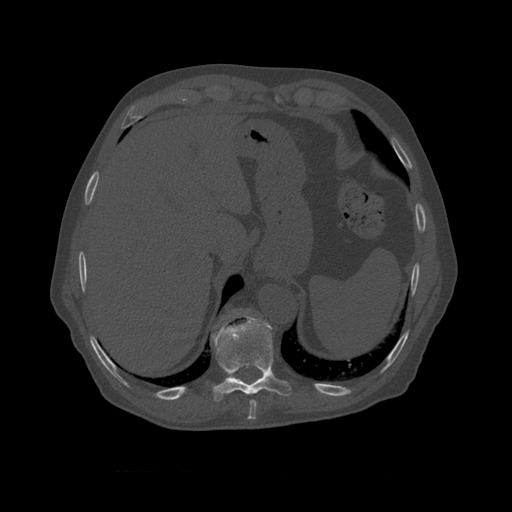
CT including the spine, one axial slice; position 423 of 450 along the scan axis; 120 kVp; bone window (W 1800 / L 400 HU); 512 × 512 image matrix. Patient age 75 years. Case-level facts recorded for this patient, not image findings: primary cancer: prostate.
Structures marked on this image (semi-automatically segmented with operator editing):
- T10 vertebra: box from (x=233, y=309) to (x=252, y=315) px
- T8 vertebra: (x=250, y=400)–(x=257, y=411)
- T9 vertebra: (x=212, y=316)–(x=292, y=397)